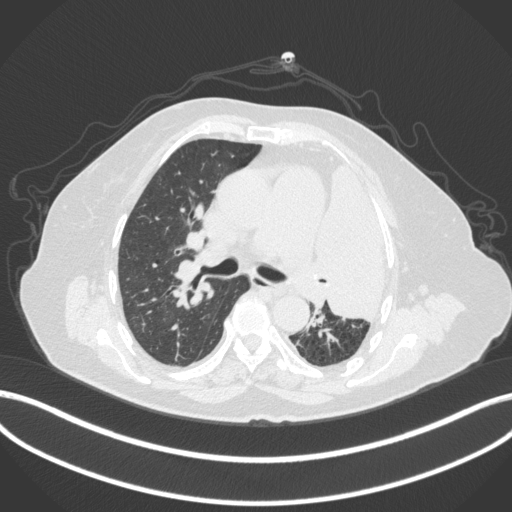
Chest CT, one axial slice. Position 241 of 399 along the scan axis. Lung window (W 1500 / L -600 HU). 512 × 512 image matrix. Female patient, age 75 years. From the clinical record (not read from this slice): clinical TNM (as recorded): T3 N3 M1.
Outlined on this slice (bounding box drawn by a radiologist):
- lung tumour (recorded histology: adenocarcinoma): bounding box [x1, y1, x2, y2] px = [311, 153, 392, 325]